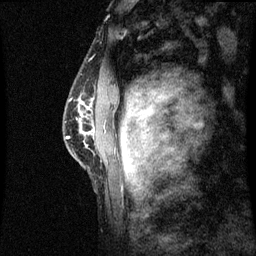
Breast MRI (dynamic contrast-enhanced), one sagittal slice. Slice 46 of 60 in the series (ordered by position). Dynamic contrast-enhanced series, image 2 of 3 at this slice position (ordered by acquisition). 1.5 T. TE 4.2 ms, TR 8.9 ms. 2 mm slice thickness. 256 × 256 image matrix, field of view 200 × 200 mm. Female patient, age 50 years. Case-level facts recorded for this patient, not image findings: setting: breast cancer imaged before/during neoadjuvant chemotherapy; receptor status: triple-negative.
Structures marked on this image (semi-automatically segmented with operator editing):
- analysis volume of interest (the breast-tissue region the enhancement analysis was run in; not a lesion): bounding box [x1, y1, x2, y2] px = [68, 86, 97, 167]
- tumour enhancement mask (voxels above the 70 % enhancement threshold inside the analysis volume of interest): [68, 102, 90, 139]